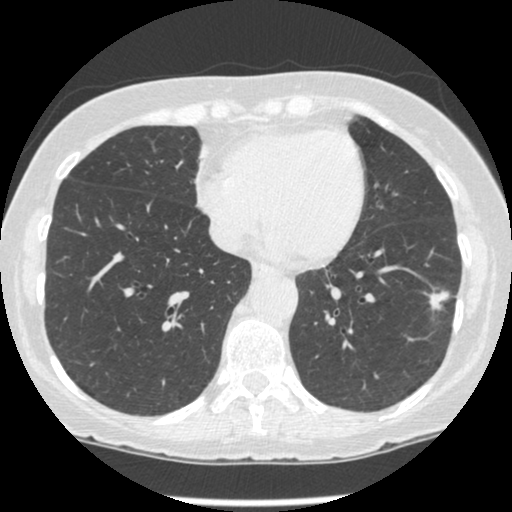
Low-dose screening chest CT, one axial slice. Slice 86 of 247 in the series (ordered by position). 120 kVp. Lung window (W 1500 / L -600 HU). 1.25 mm slice thickness. 512 × 512 image matrix.
Annotated regions visible in this slice (outlined manually by an expert reader):
- lesion 1 (tumor, lower lobe of left lung): bounding box (x1, y1, x2, y2) in pixels: (428, 290, 450, 310)